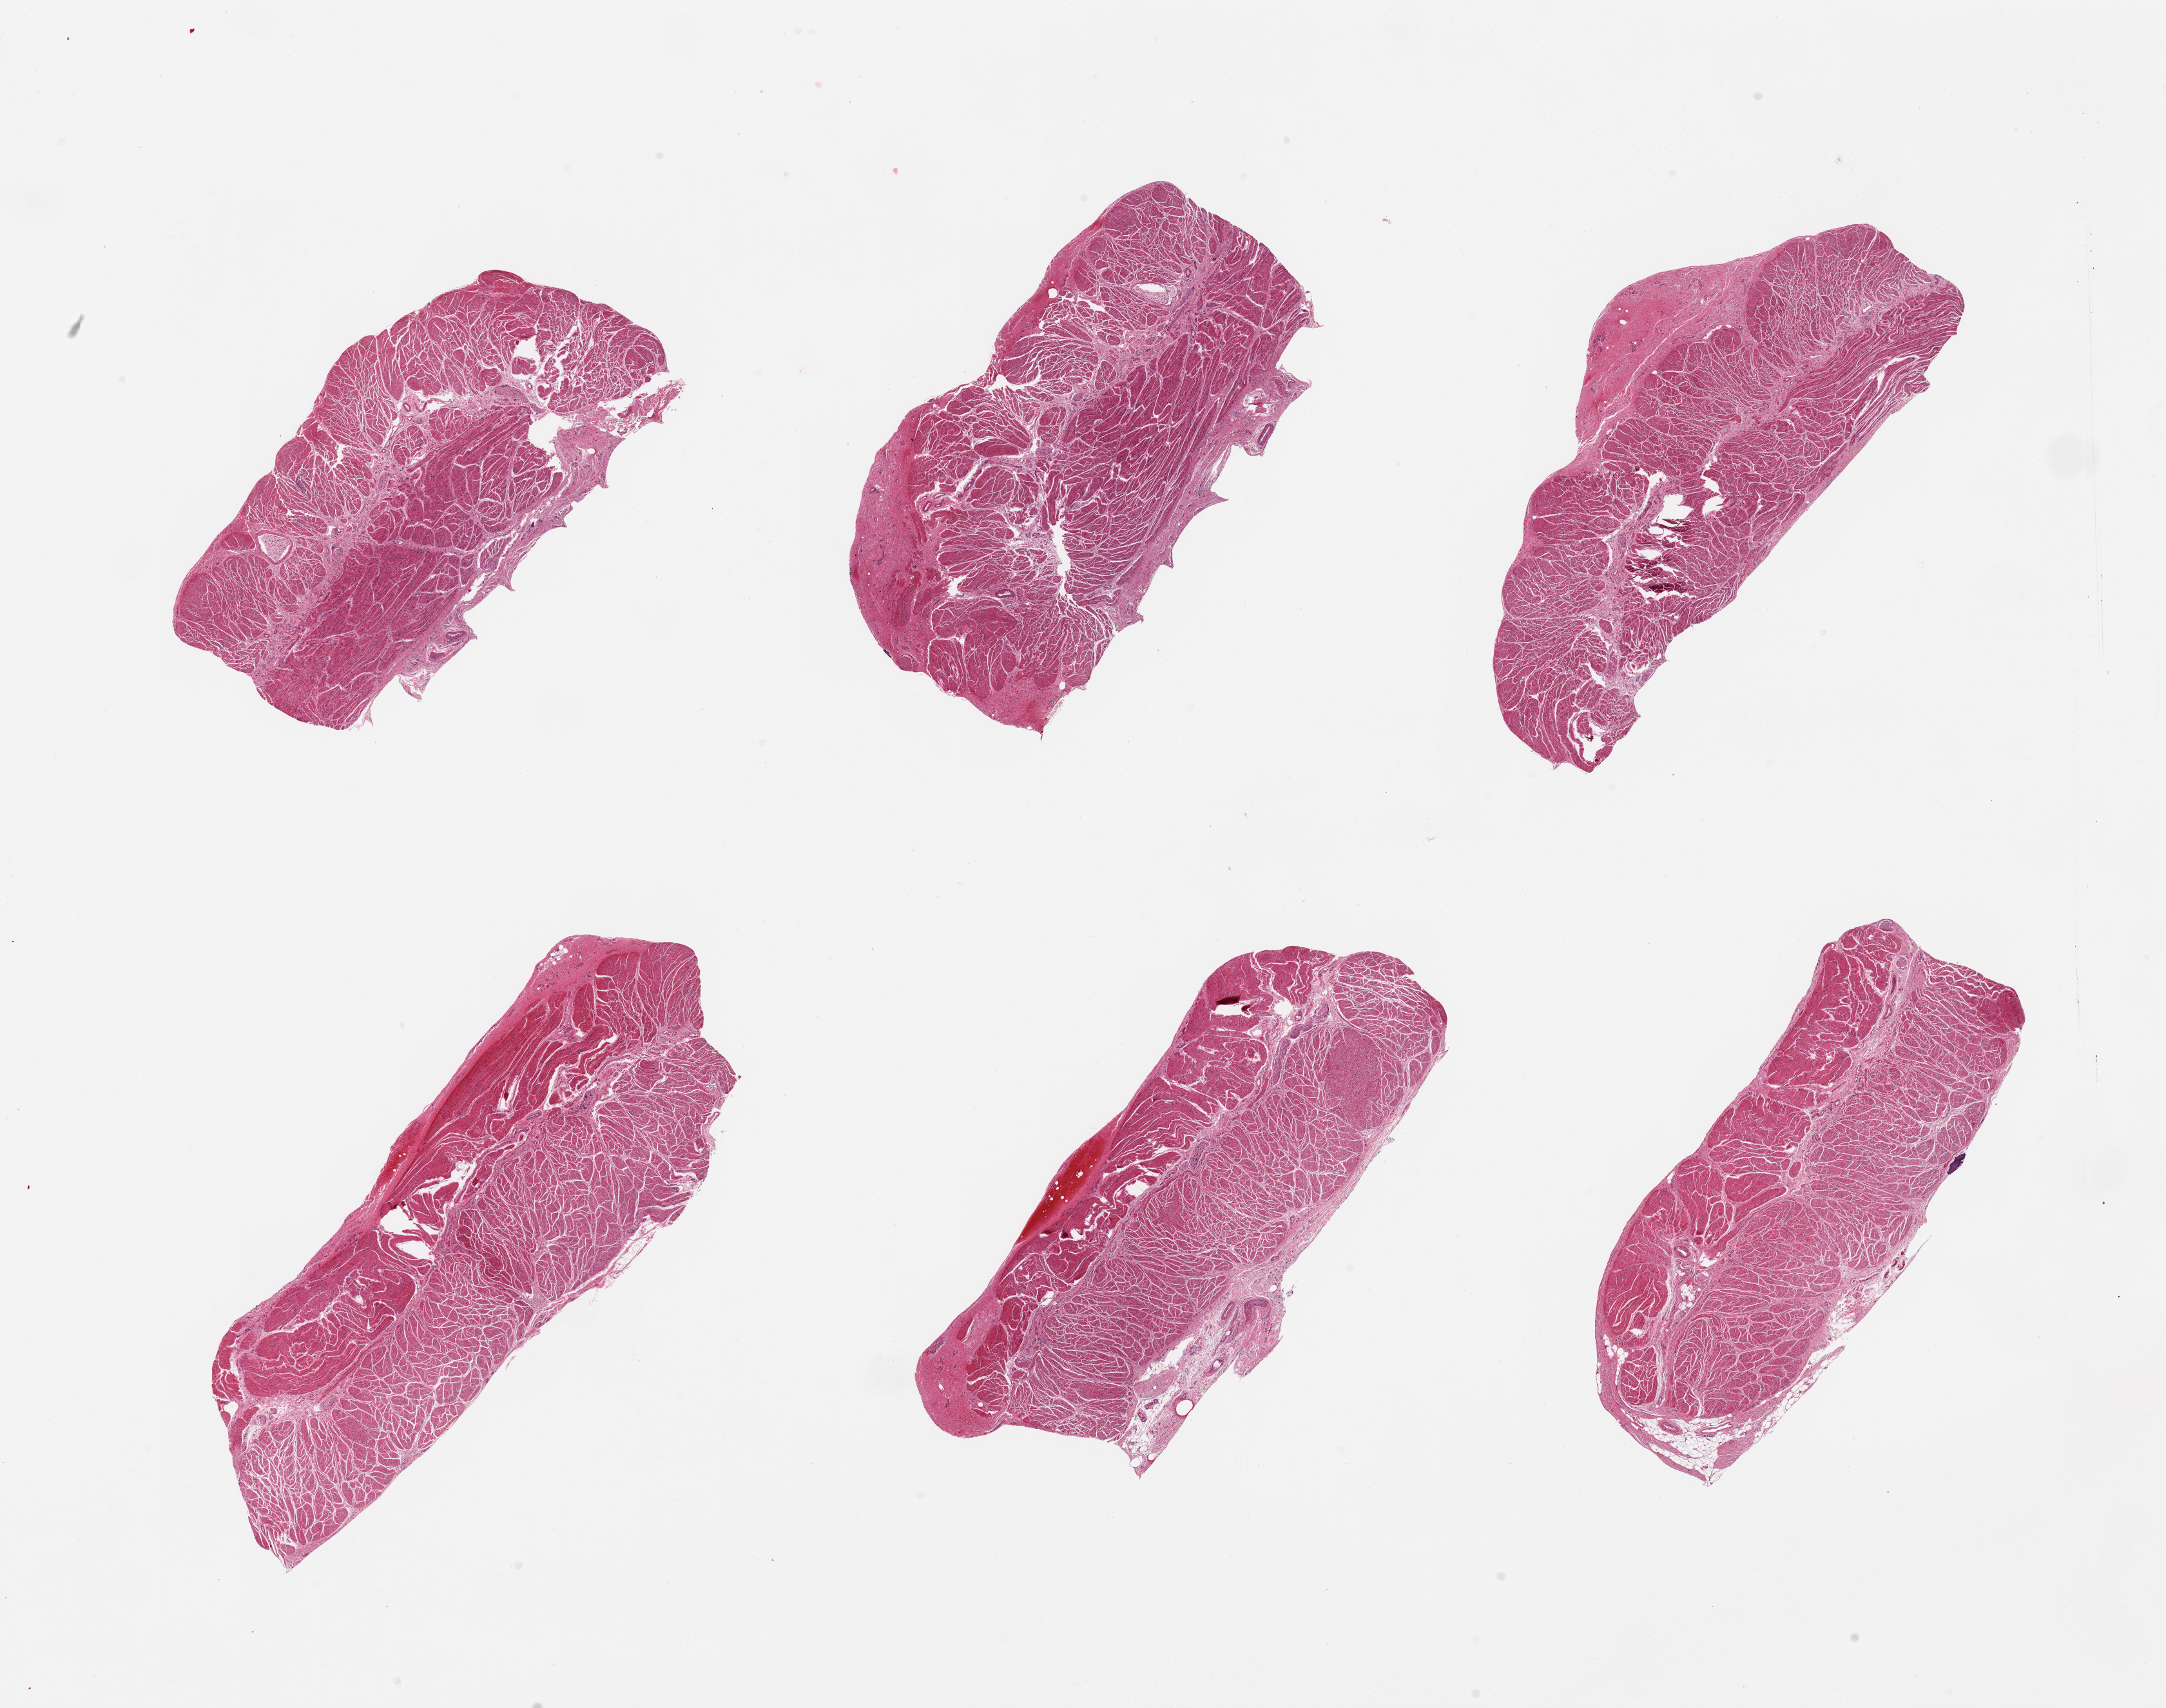
Whole-slide image, H&E stain — shown as a low-resolution overview of the whole scanned area (about 26.6 x 21.0 mm, from a 20x scan); PAXgene-fixed, paraffin-embedded tissue; target tissue: gastroesophageal junction; donor tissue sample. Donor: female.
Review note (as recorded): 6 pieces; well trimmed.